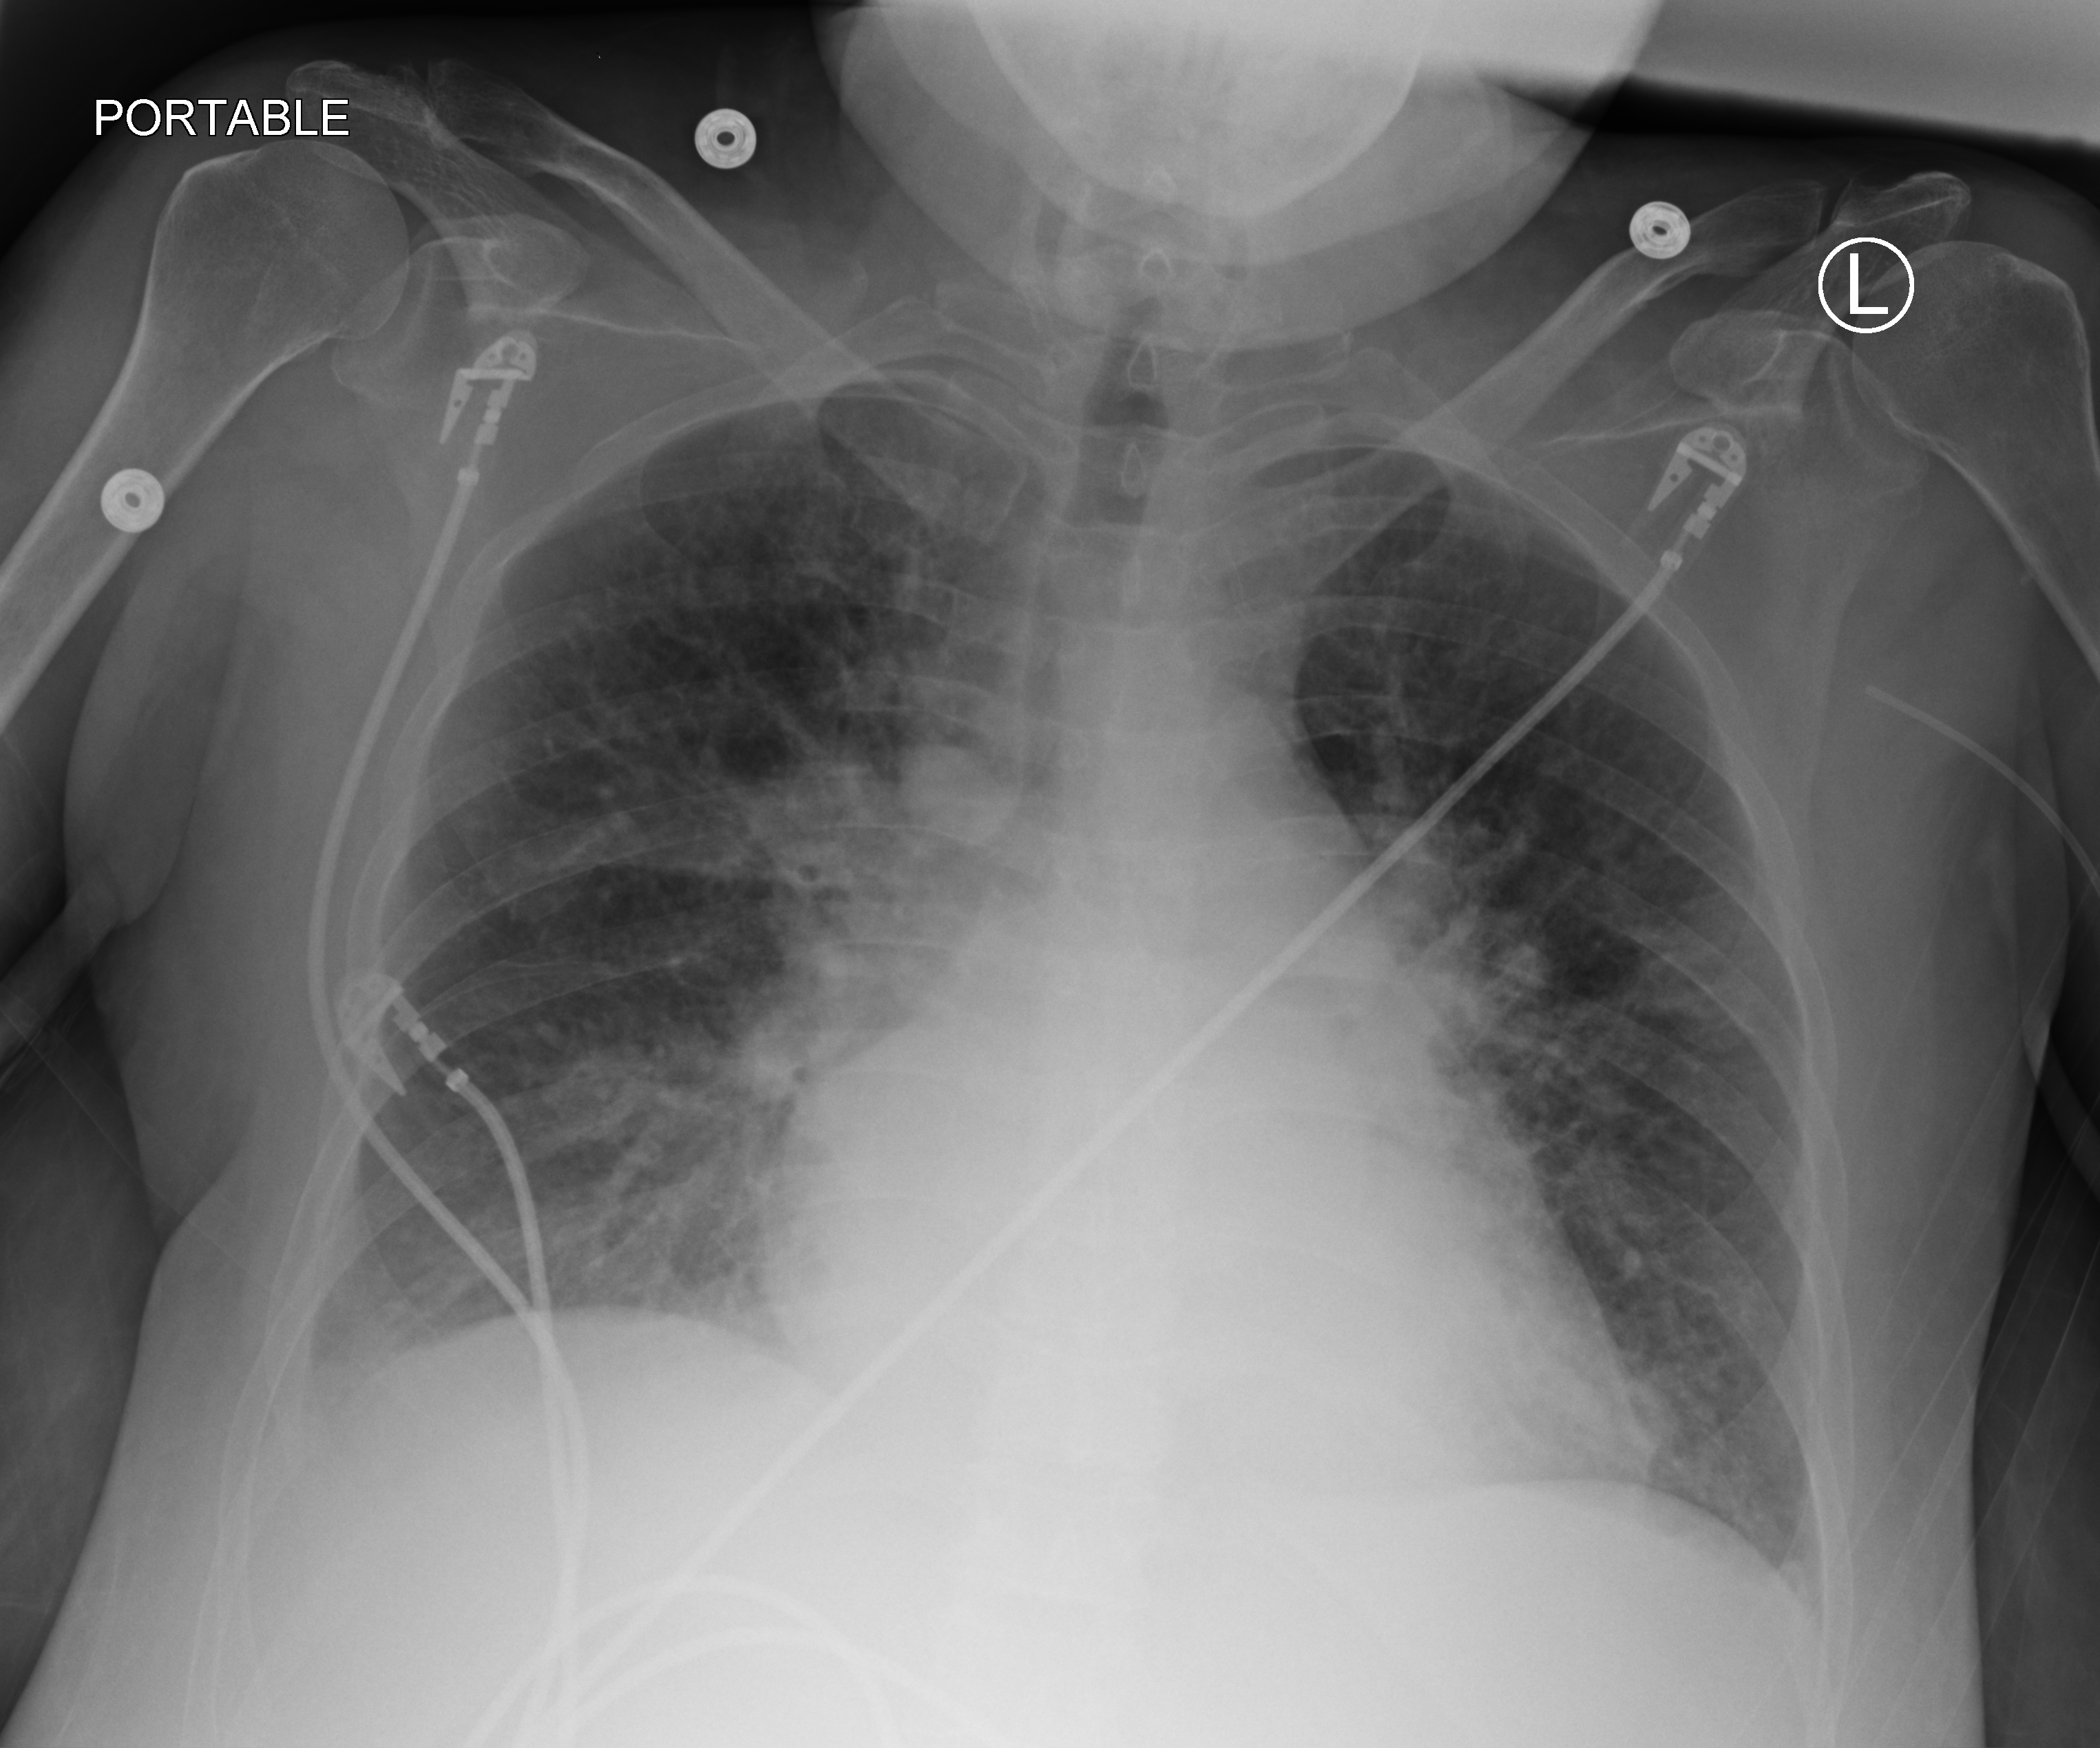
Bedside chest radiograph (computed radiography), anteroposterior (AP) projection. Patient hospitalised with COVID-19; female, aged 18–59 years.
From the hospital-stay record, not from the radiograph (when in the stay this image was taken is not recorded): admitted to intensive care during this hospital stay: no.